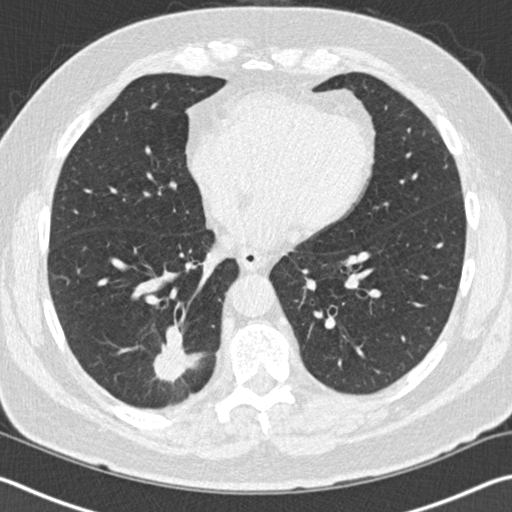
Low-dose screening chest CT, one axial slice. Slice 43 of 141 in the series (ordered by position). Reconstruction kernel B30f. Lung window (W 1500 / L -600 HU). 512 × 512 image matrix, field of view 344 × 344 mm.
Outlined on this slice (expert manual segmentation):
- lesion 1 (tumor, lower lobe of right lung): bounding box (x1, y1, x2, y2) in pixels: (153, 326, 193, 382)